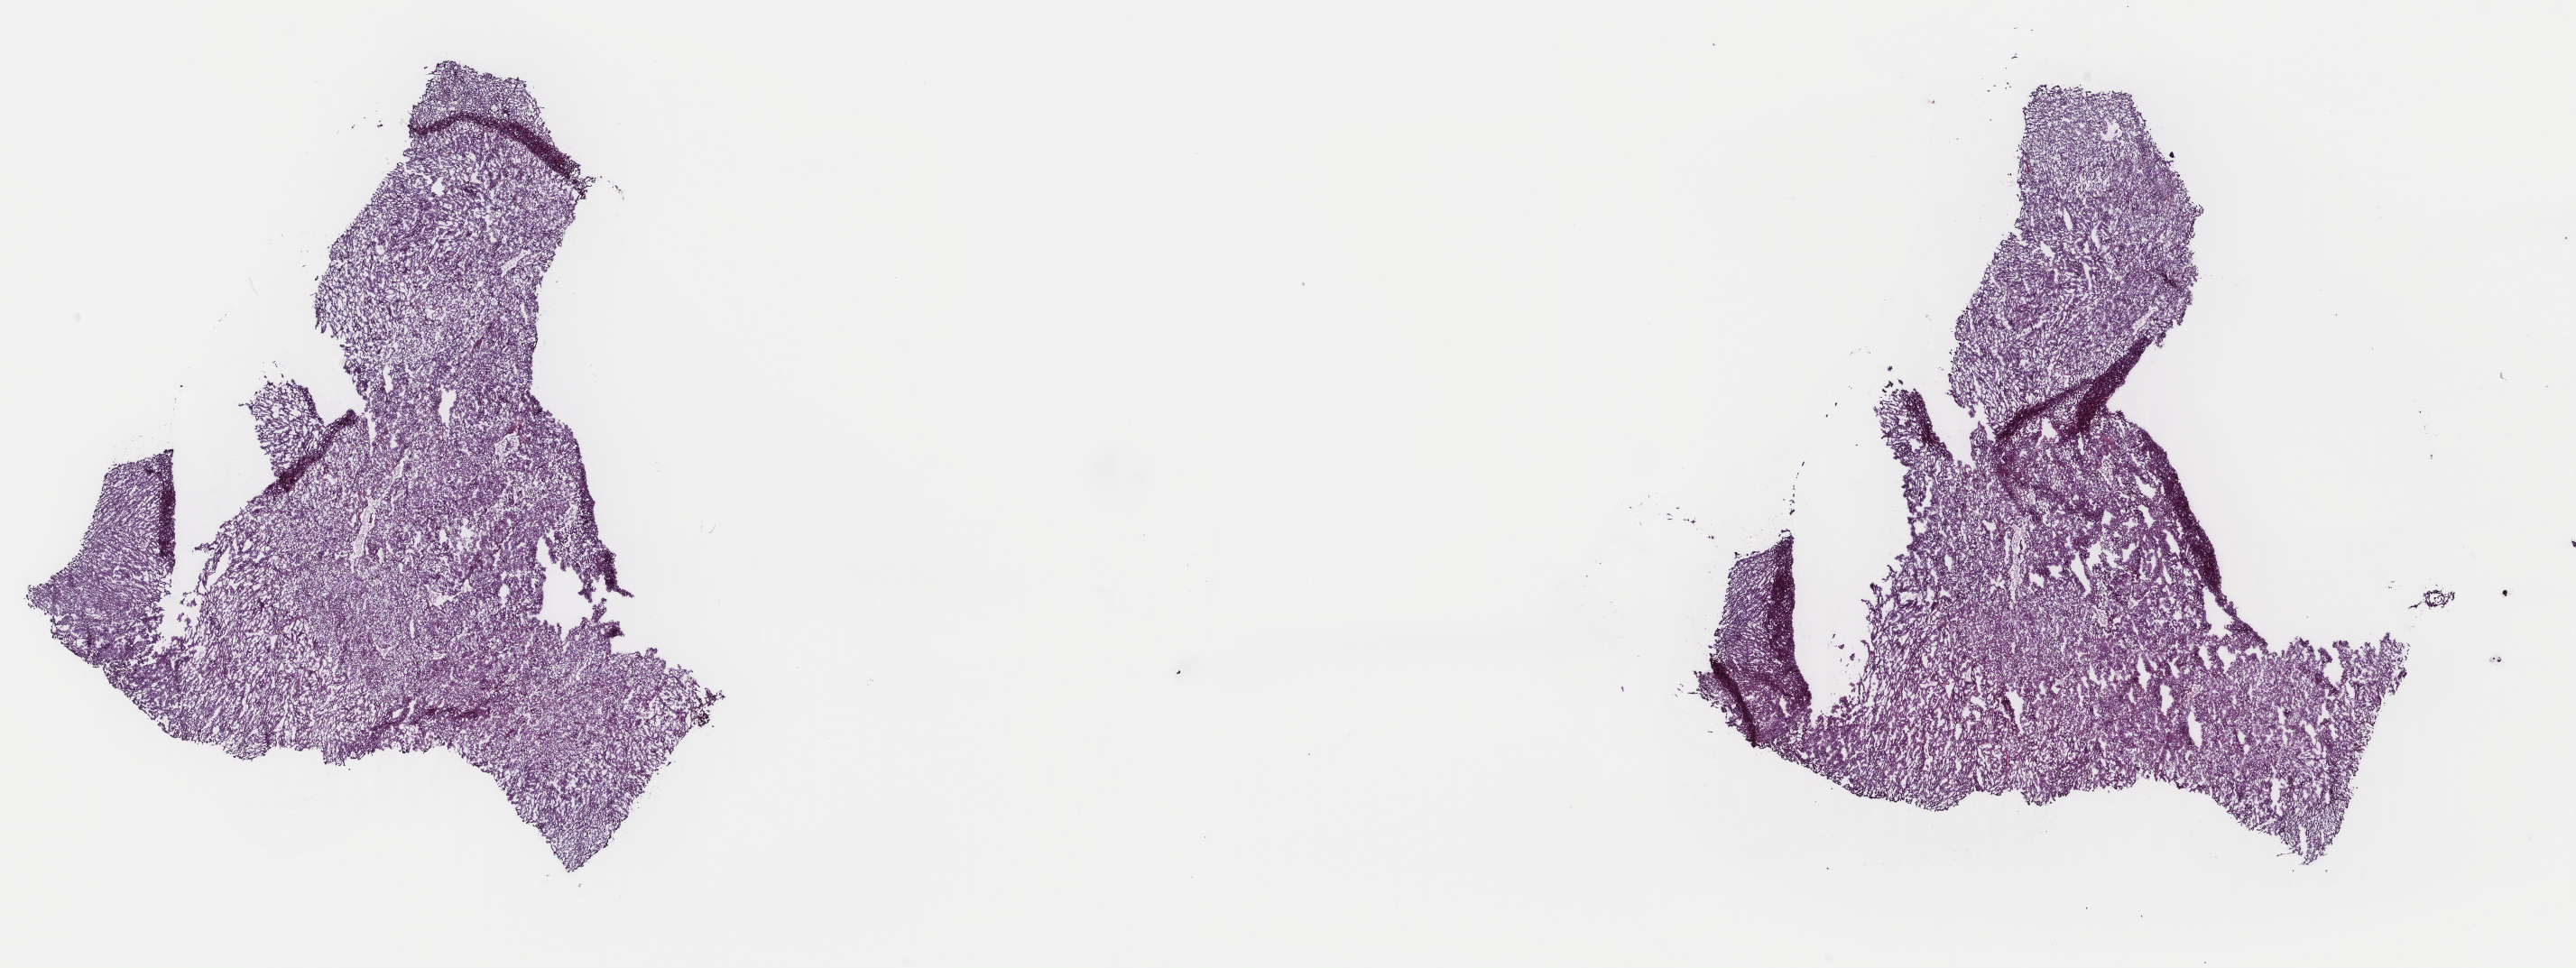
Digitized H&E tissue section (whole slide), low-resolution overview of the scanned area, about 22.7 x 8.5 mm. Frozen section. Adrenal cortex, primary tumour sample. Patient: female, age at initial diagnosis 23 years. Slide review estimates, as recorded: tumour cells 100%, tumour nuclei 80%, normal cells 0%, stromal cells 0%, necrosis 0%. Infiltration values recorded for this section: lymphocyte infiltration 2%, monocyte infiltration 0%, neutrophil infiltration 0%.
* diagnosis: Adrenal cortical carcinoma
* laterality: left
* lymph nodes positive (case pathology): 0 of 4 examined